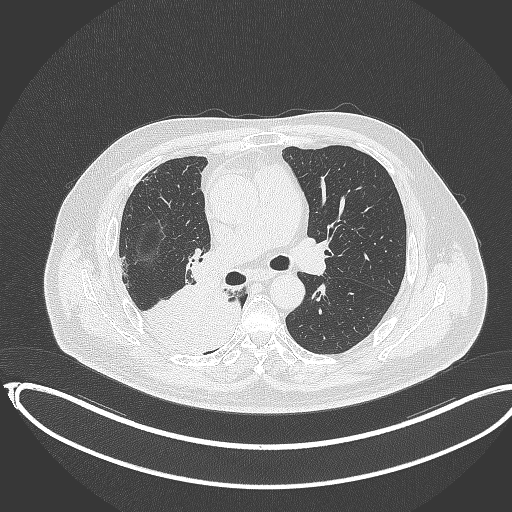
Chest CT, one axial slice; slice 208 of 403 in the series (ordered by position); reconstruction kernel B70f; 120 kVp; lung window (W 1500 / L -600 HU); 512 × 512 image matrix. Male patient, age 68 years. From the clinical record (not read from this slice): clinical TNM (as recorded): T2a N0 M0.
Structures marked on this image (bounding box drawn by a radiologist):
- lung tumour (recorded histology: adenocarcinoma): box from (x=147, y=275) to (x=243, y=356) px